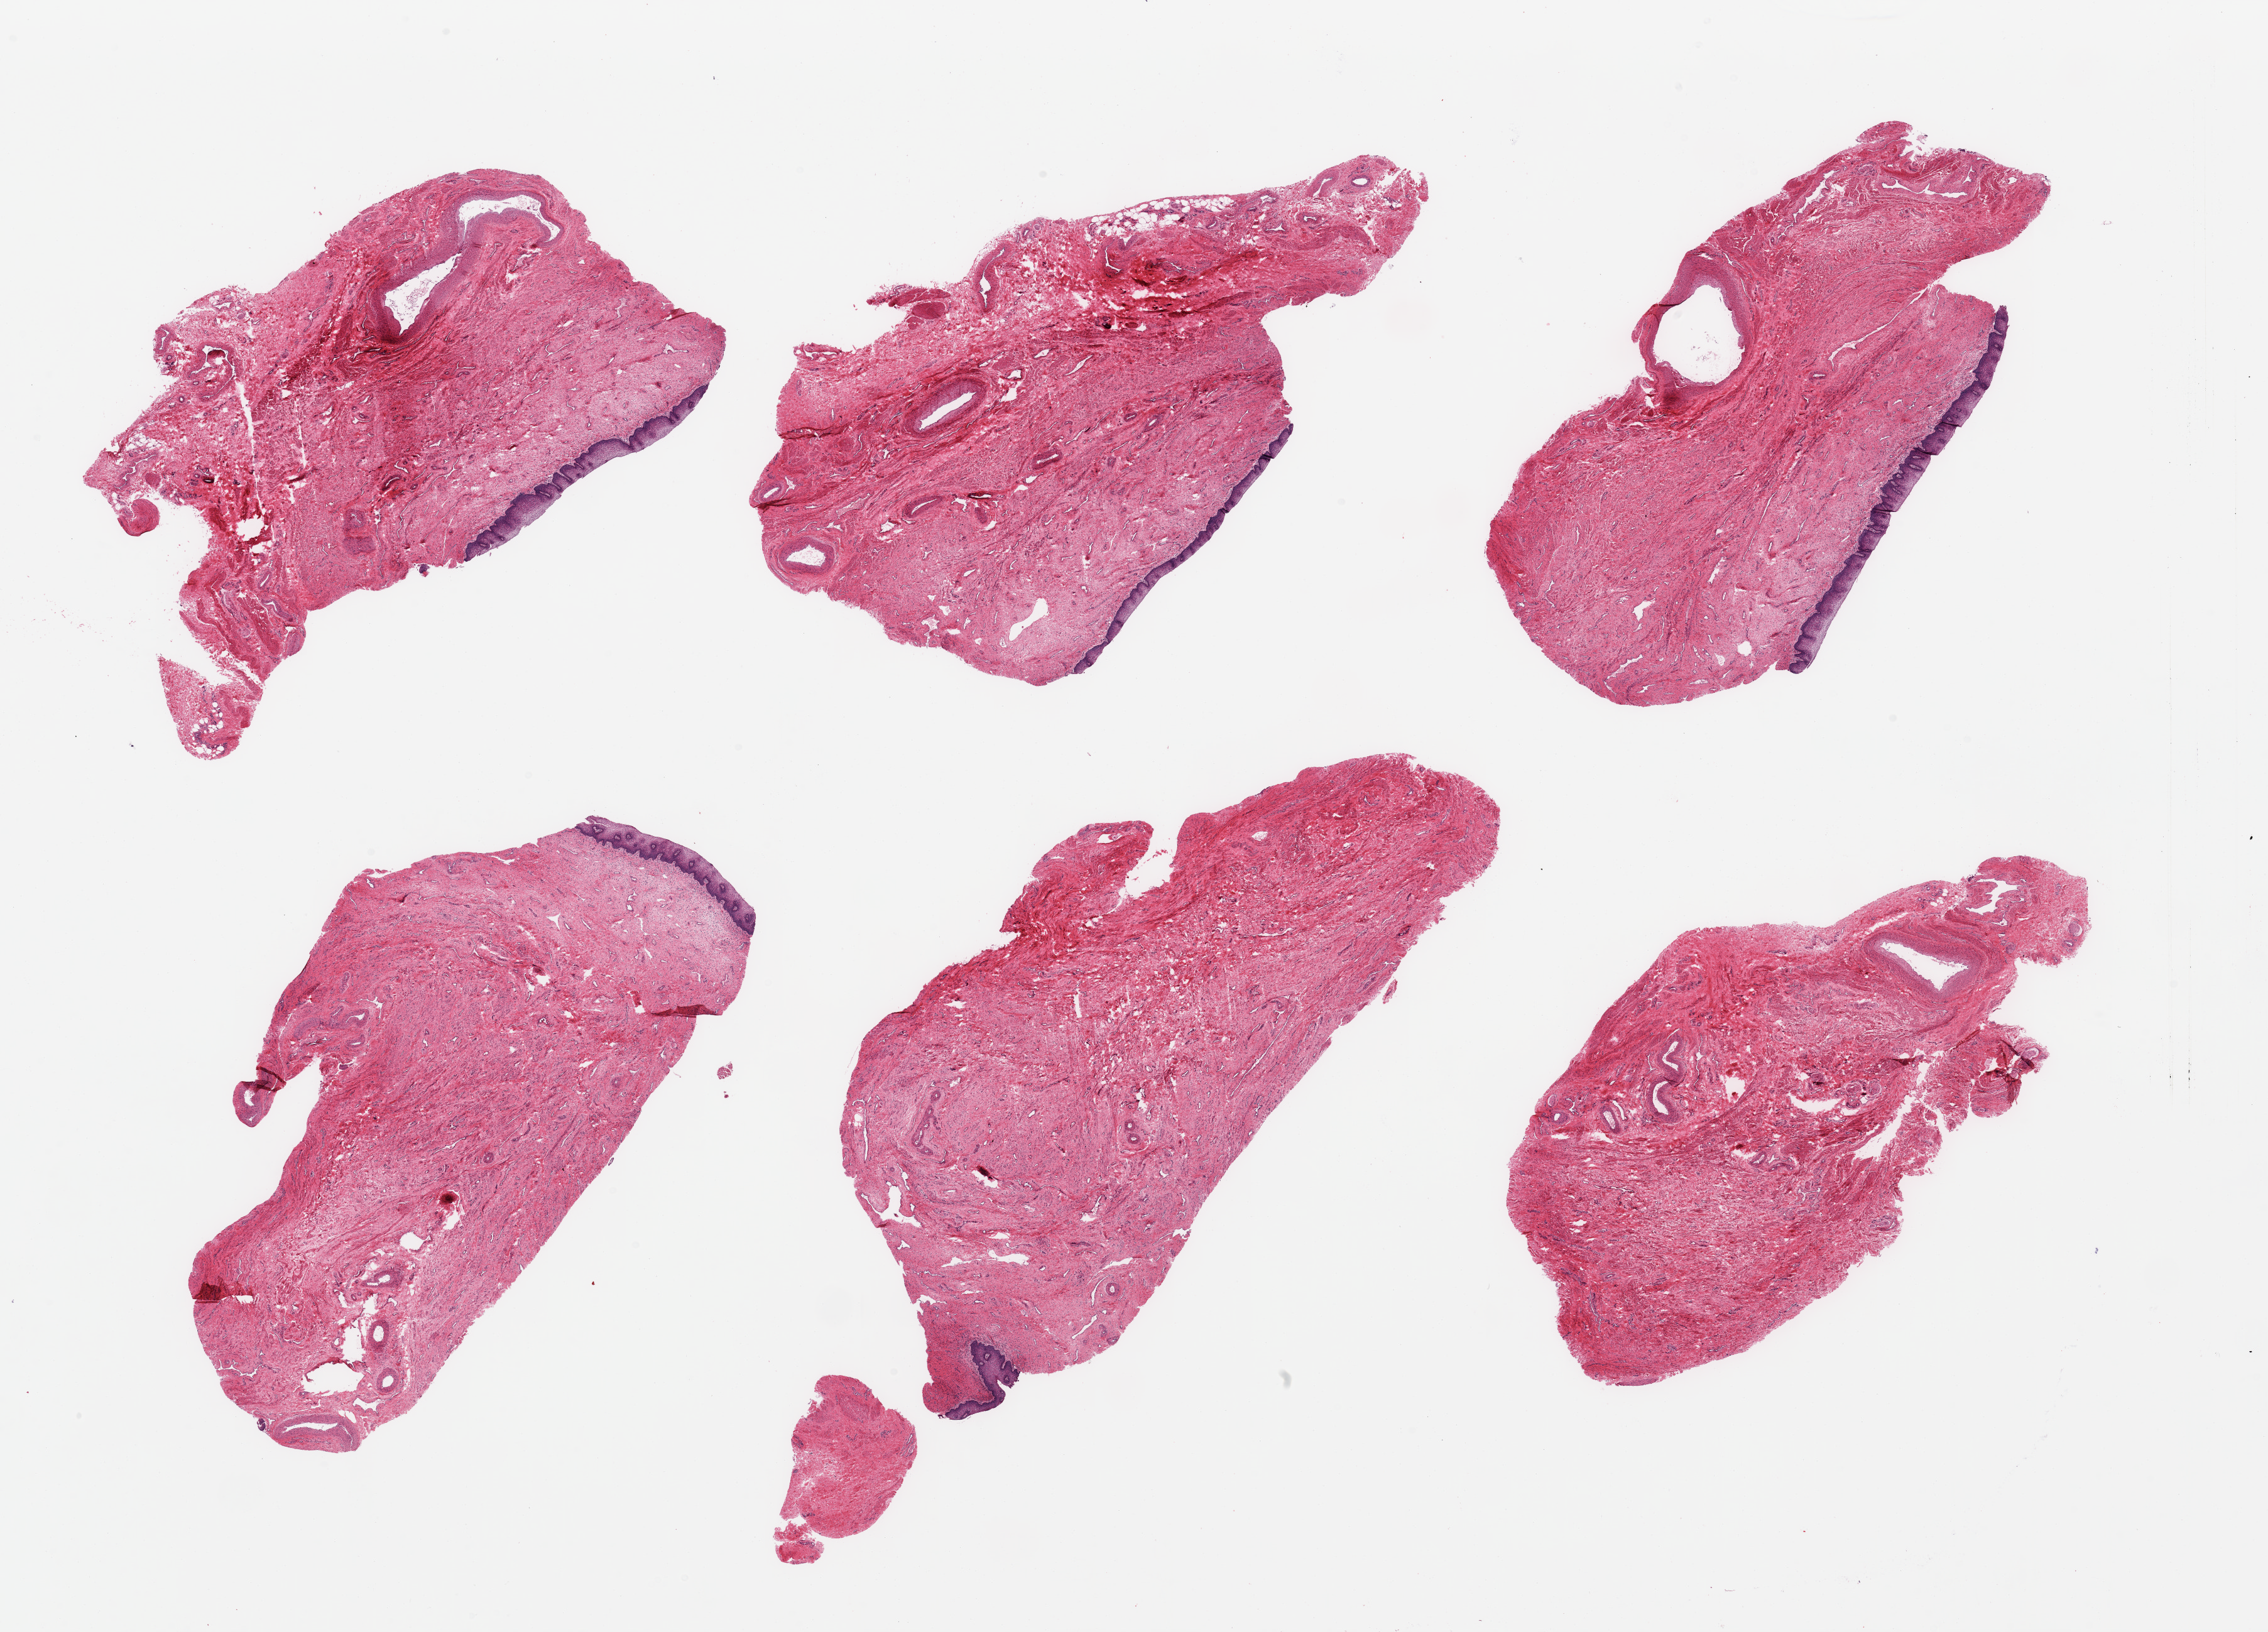
Haematoxylin and eosin whole-slide image — whole scanned area (about 28.5 x 20.5 mm) shown as a low-resolution overview, PAXgene-fixed paraffin-embedded (PFPE) section, sampled site (target tissue): vagina, tissue donor sample. Donor: female.
Pathologist's review note for this sample: 6 pieces; one piece completely devoid of squamous epithelium; well preserved lamina propria.